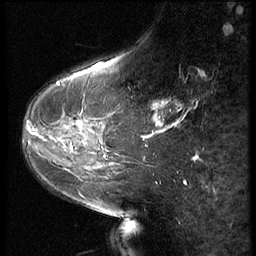
Breast MRI (dynamic contrast-enhanced), one sagittal slice; slice 22 of 66 in the series (ordered by position); 3 images stored at this slice position (order not interpretable as contrast timing); 1.5 T; TE 4.2 ms, TR 9 ms; 2.5 mm slice thickness; 256 × 256 image matrix, field of view 180 × 180 mm. Patient: female, 54 years. Case-level facts recorded for this patient, not image findings: setting: breast cancer imaged before/during neoadjuvant chemotherapy; receptor status: HR-positive, HER2-negative.
Structures marked on this image (semi-automatic segmentation, software-assisted and operator-edited):
- analysis volume of interest (the breast-tissue region the enhancement analysis was run in; not a lesion): bounding box (x1, y1, x2, y2) in pixels: (26, 110, 94, 159)
- tumour enhancement mask (voxels above the 140 % enhancement threshold inside the analysis volume of interest): (37, 124, 81, 135)